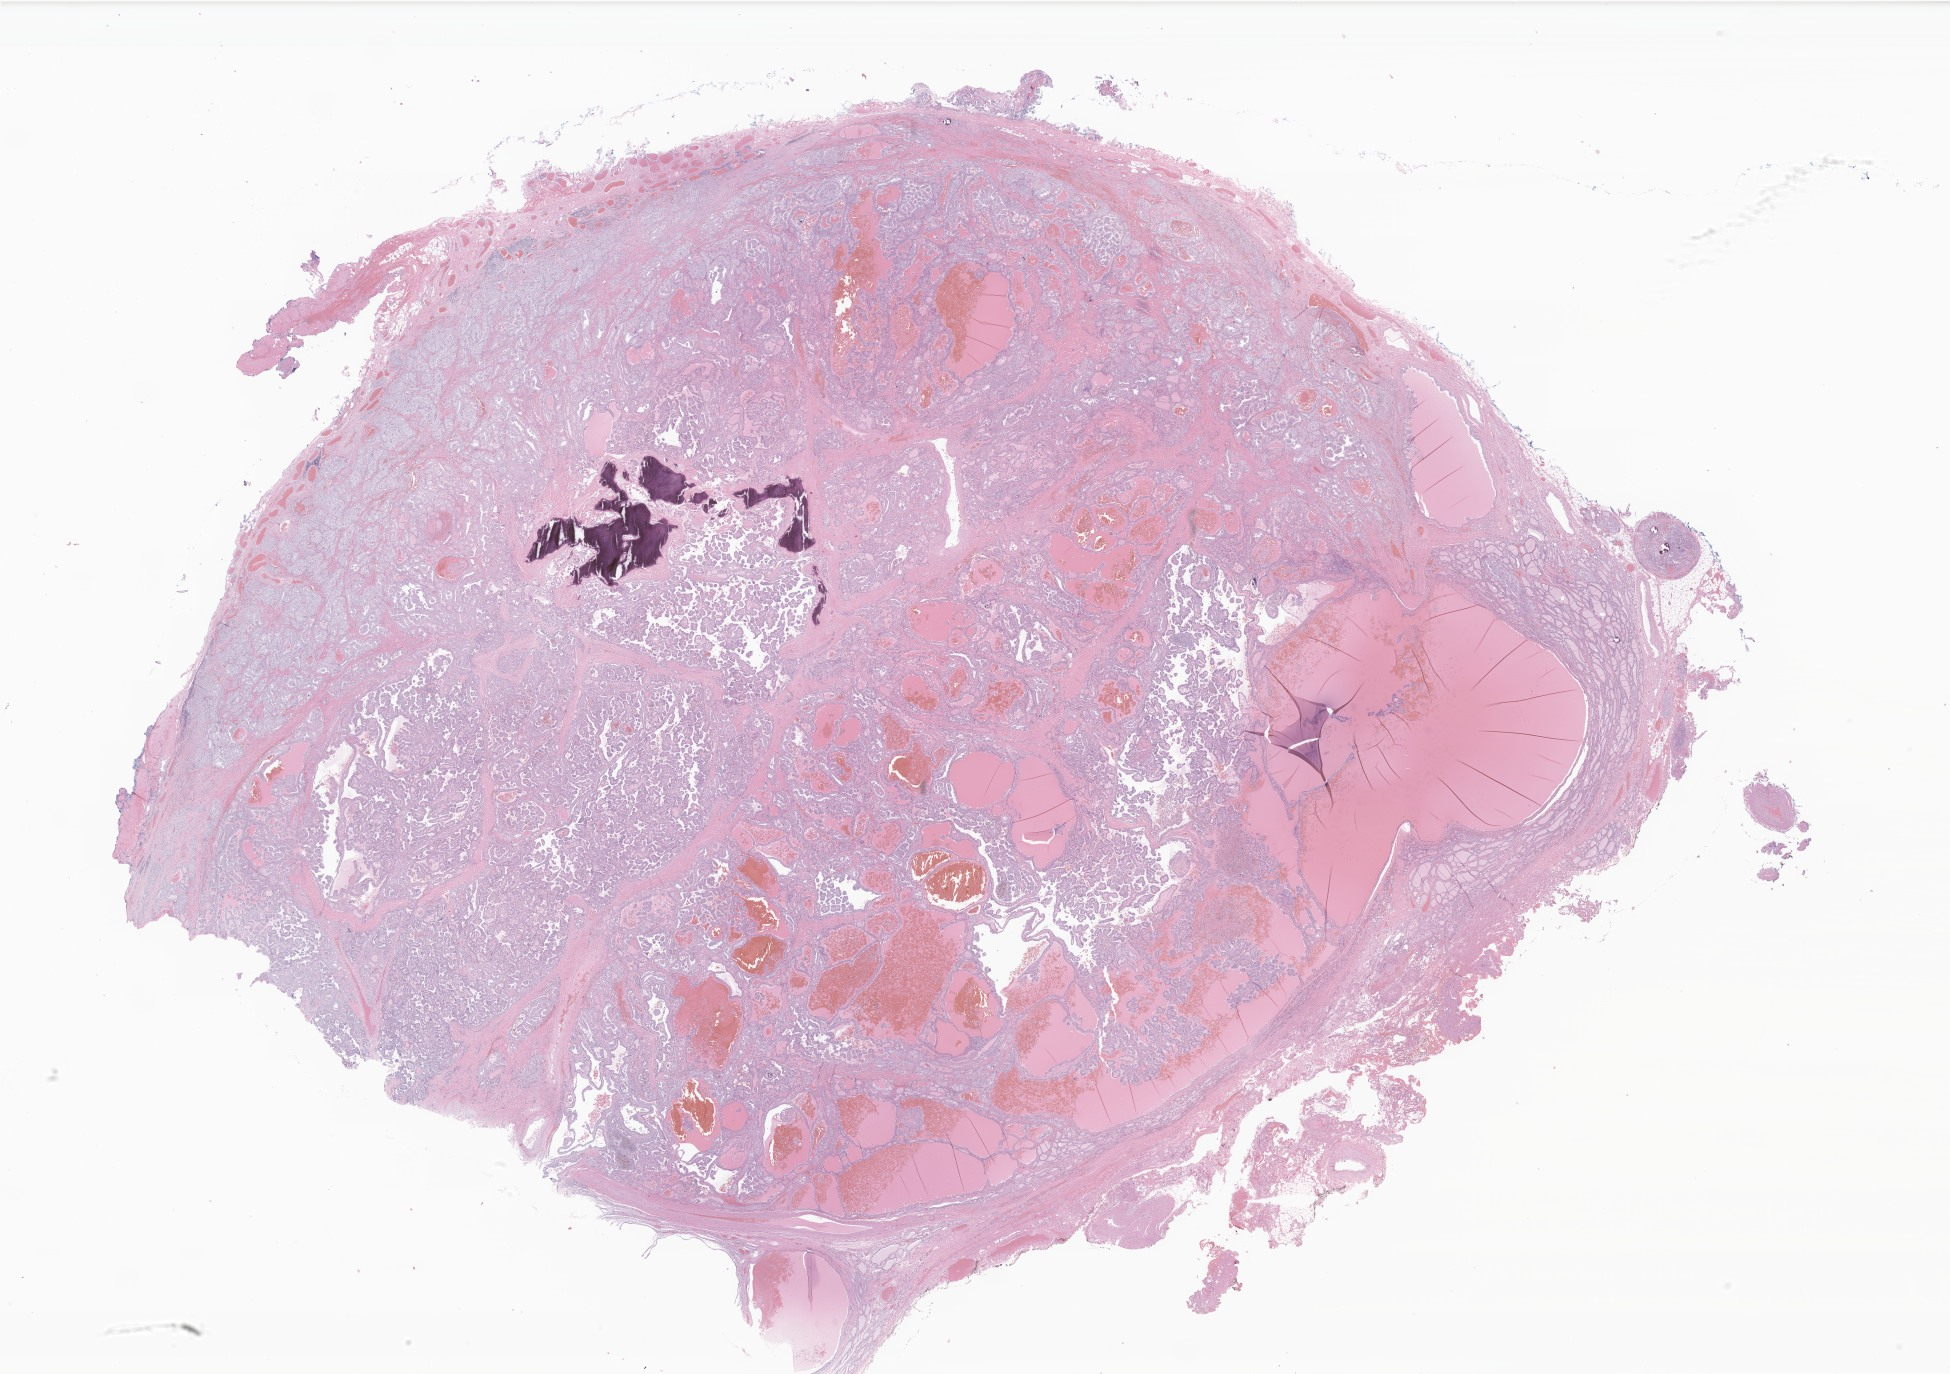
Whole-slide image, hematoxylin and eosin (H&E) stain of tumor tissue from the thyroid, shown as a low-resolution overview of the whole scanned area (about 32.9 x 23.2 mm). FFPE section. Patient: male, age 173 months (14 years 5 months).
Diagnosis (ICD-O-3 morphology term): Neoplasm, uncertain whether benign or malignant.